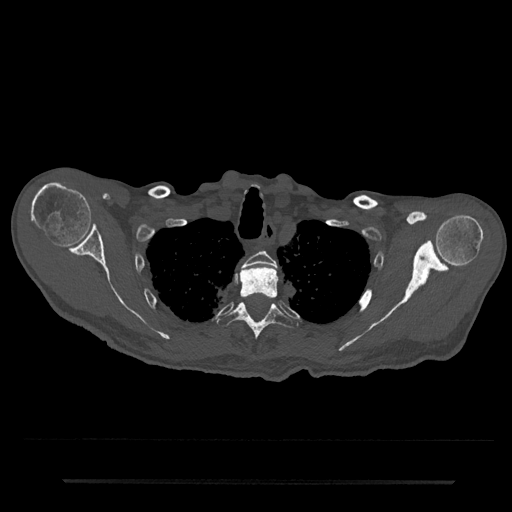
CT including the spine, one axial slice. Slice 645 of 797 in the series (ordered by position). Reconstruction kernel Br40s/3. Bone window (W 1800 / L 400 HU). 512 × 512 image matrix, field of view 427 × 427 mm. Male patient, age 74 years. From the clinical record (not read from this slice): primary cancer: prostate.
Outlined on this slice (semi-automatic segmentation, software-assisted and operator-edited):
- T2 vertebra: bounding box <242,251,277,268> (left, top, right, bottom; pixels)
- T3 vertebra: <239,265,278,299>
- T4 vertebra: <217,302,298,341>